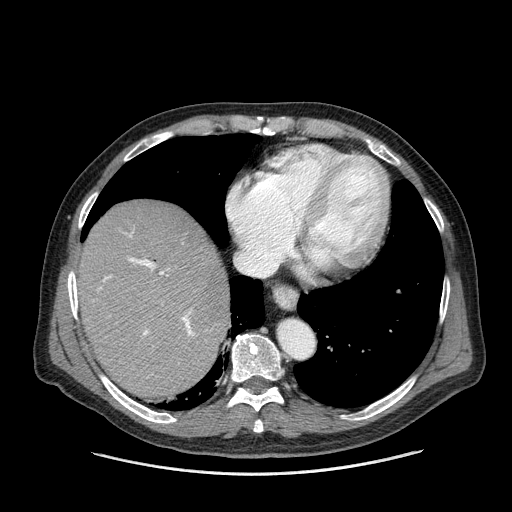
Contrast-enhanced abdominal CT (liver protocol), one axial slice; position 130 of 180 along the scan axis; reconstruction kernel STANDARD; one of 2 acquisitions stored at this slice position; soft-tissue window (W 400 / L 40 HU); 2.5 mm slice thickness; 512 × 512 image matrix, field of view 420 × 420 mm. From the clinical record (not read from this slice): diagnosis: hepatocellular carcinoma (patient treated with transarterial chemoembolisation; whether this scan precedes or follows treatment is not stated here); TNM stage (as recorded): Stage-II; Child-Pugh class: A; tumour differentiation: well differentiated; tumour size: 2.8 cm.
Annotated regions visible in this slice (semi-automatic segmentation, software-assisted and operator-edited):
- abdominal aorta: bounding box (x1, y1, x2, y2) in pixels: (279, 321, 314, 358)
- liver parenchyma outside the tumour (the mass and vessels are separate outlines, so this box may not span the whole liver): (80, 199, 228, 396)
- liver vessels: (103, 235, 195, 336)